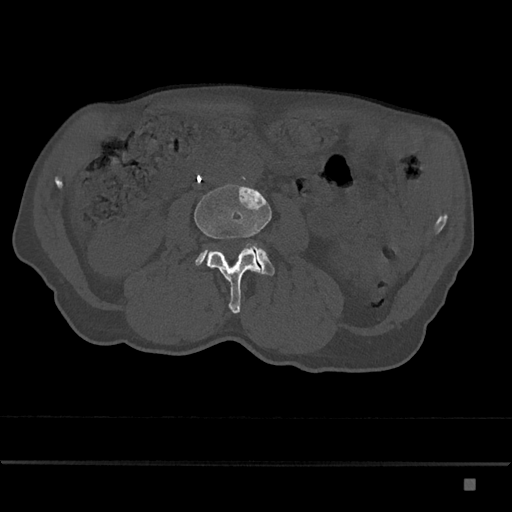
CT including the spine, one axial slice. Position 388 of 797 along the scan axis. Bone window (W 1800 / L 400 HU). 0.5 mm slice thickness. 512 × 512 image matrix. Male patient, age 72 years. From the clinical record (not read from this slice): primary cancer: prostate.
Annotated regions visible in this slice (semi-automatic segmentation, software-assisted and operator-edited):
- L3 vertebra: bounding box (x1, y1, x2, y2) in pixels: (194, 184, 272, 314)
- L4 vertebra: (195, 243, 275, 276)